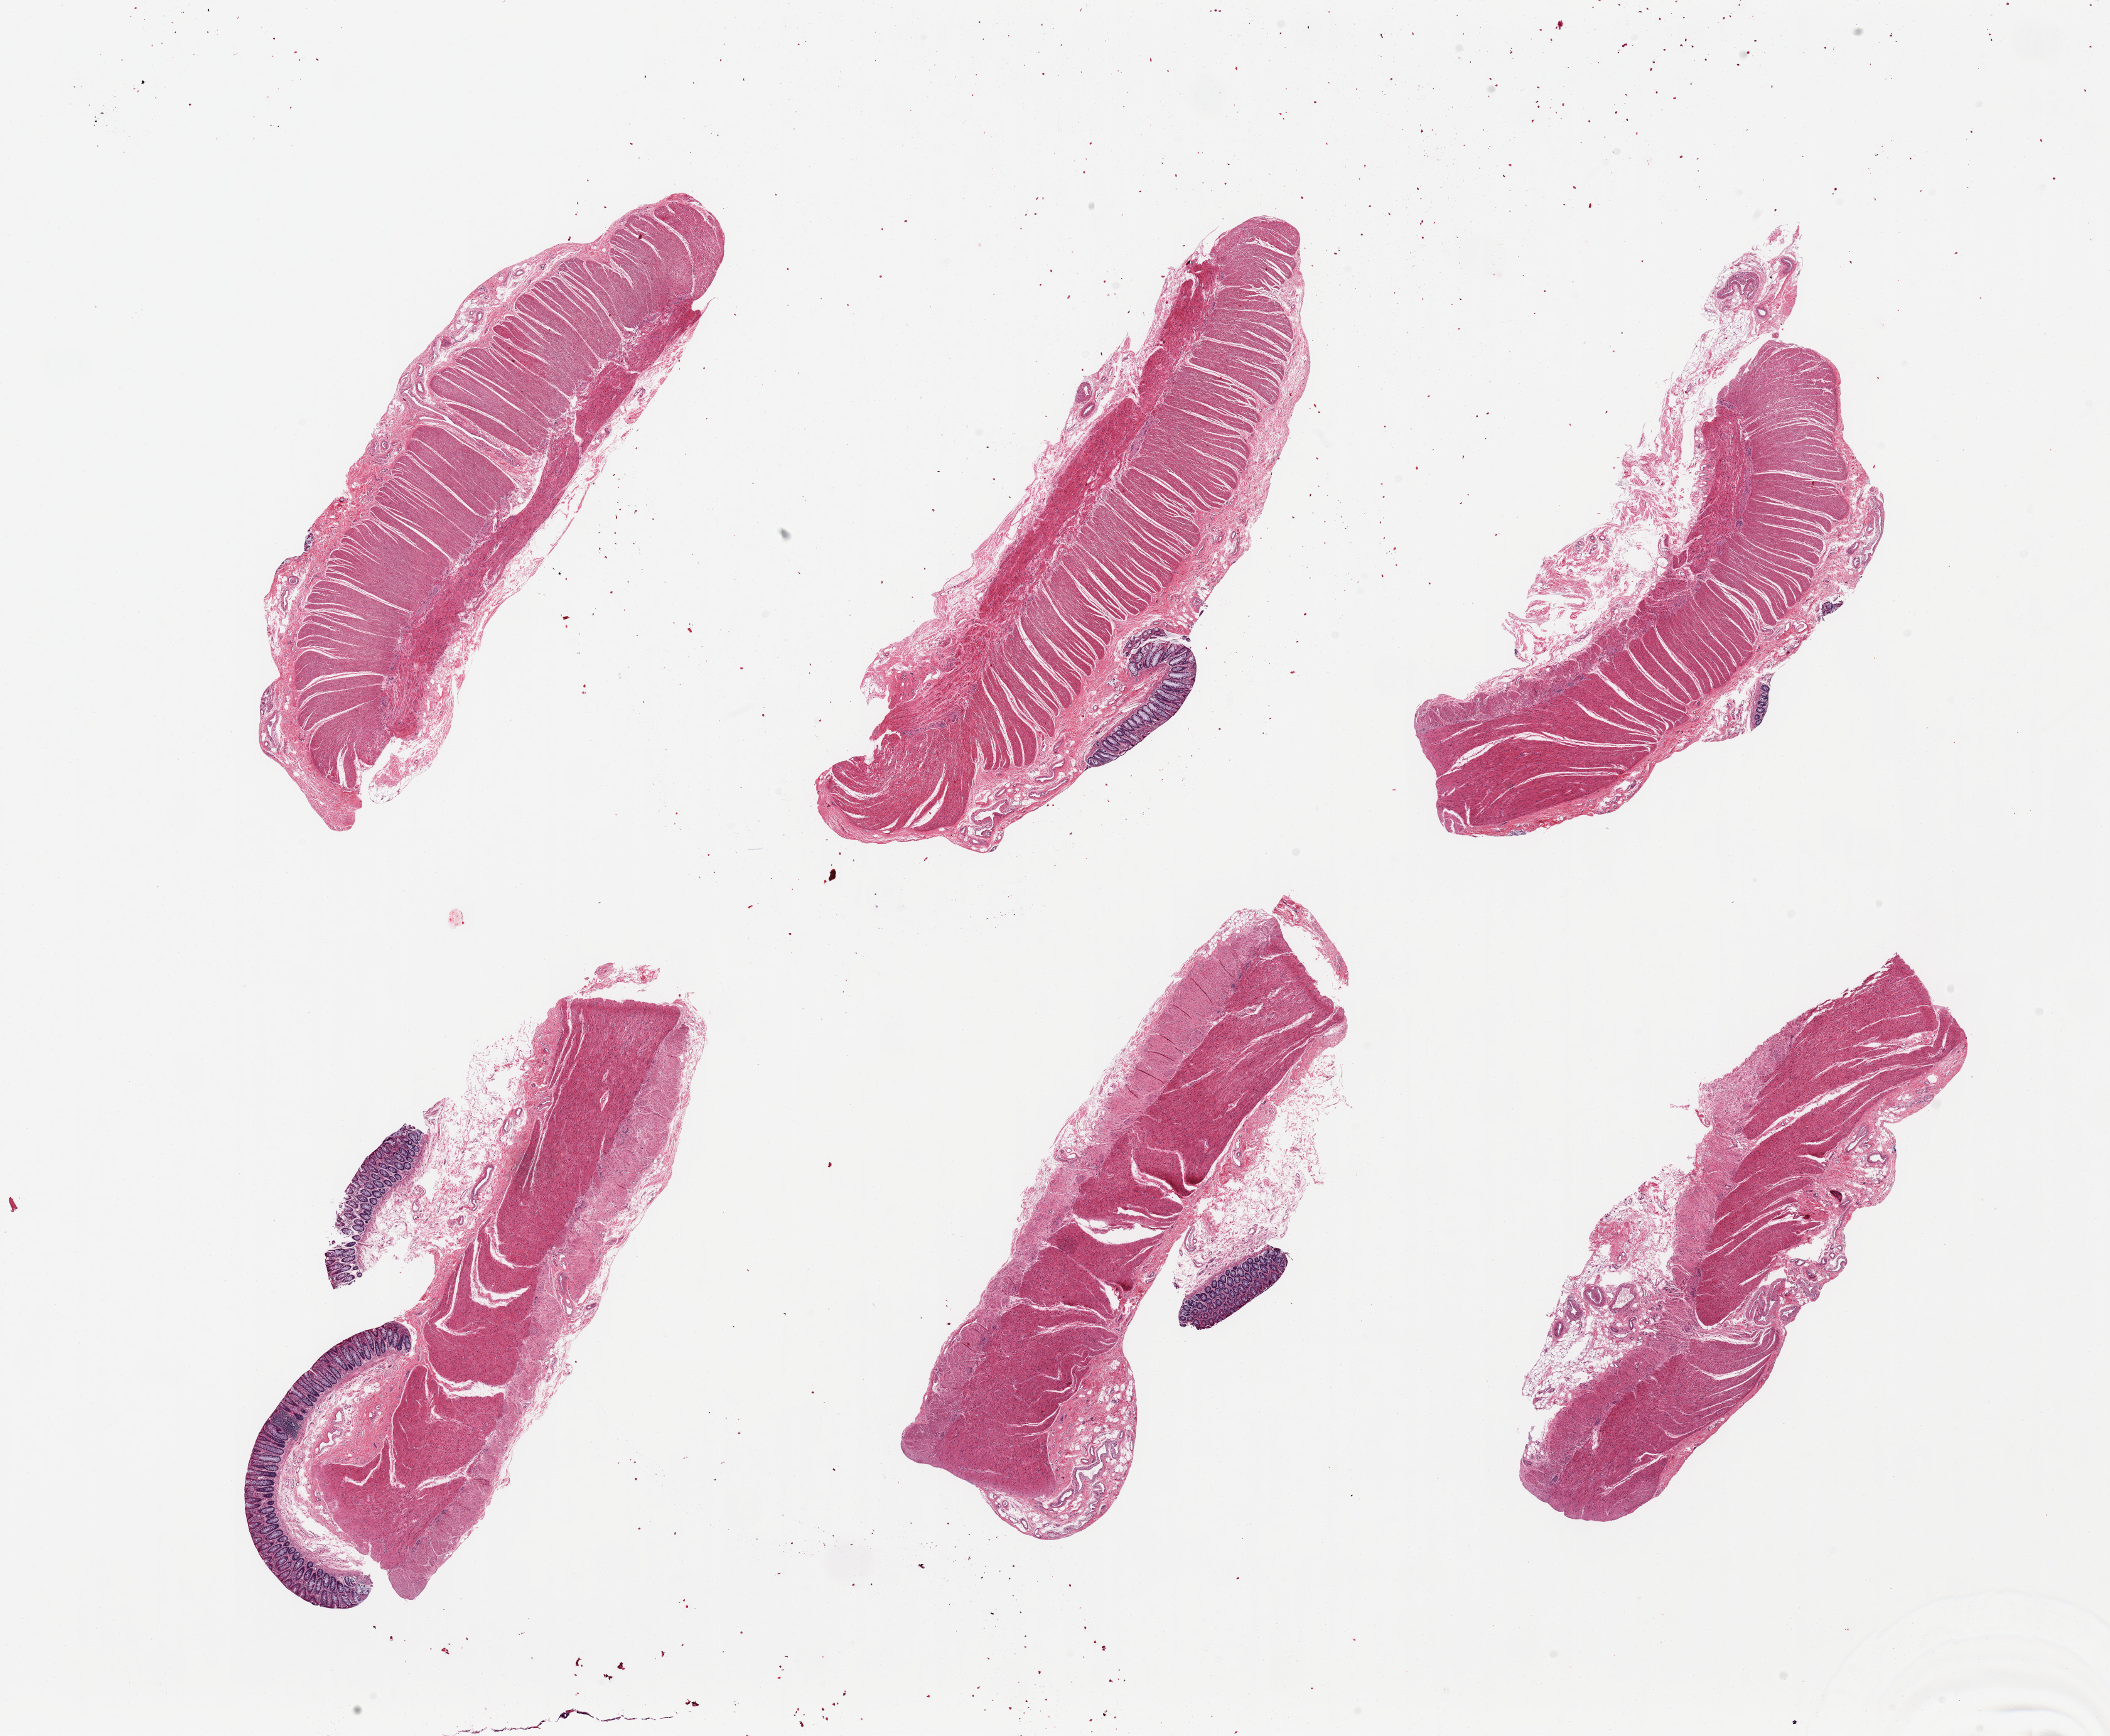
Whole-slide image, H&E stain — low-resolution overview of the scanned area, about 26.6 x 21.9 mm (acquisition: 20x scan), PAXgene-fixed, paraffin-embedded tissue, section of sigmoid colon (target tissue), donor tissue sample. Male donor.
Reviewer comment on this tissue sample: 6 pieces; predominantly target muscularis with portions of residual attached submucosa and mucosa.